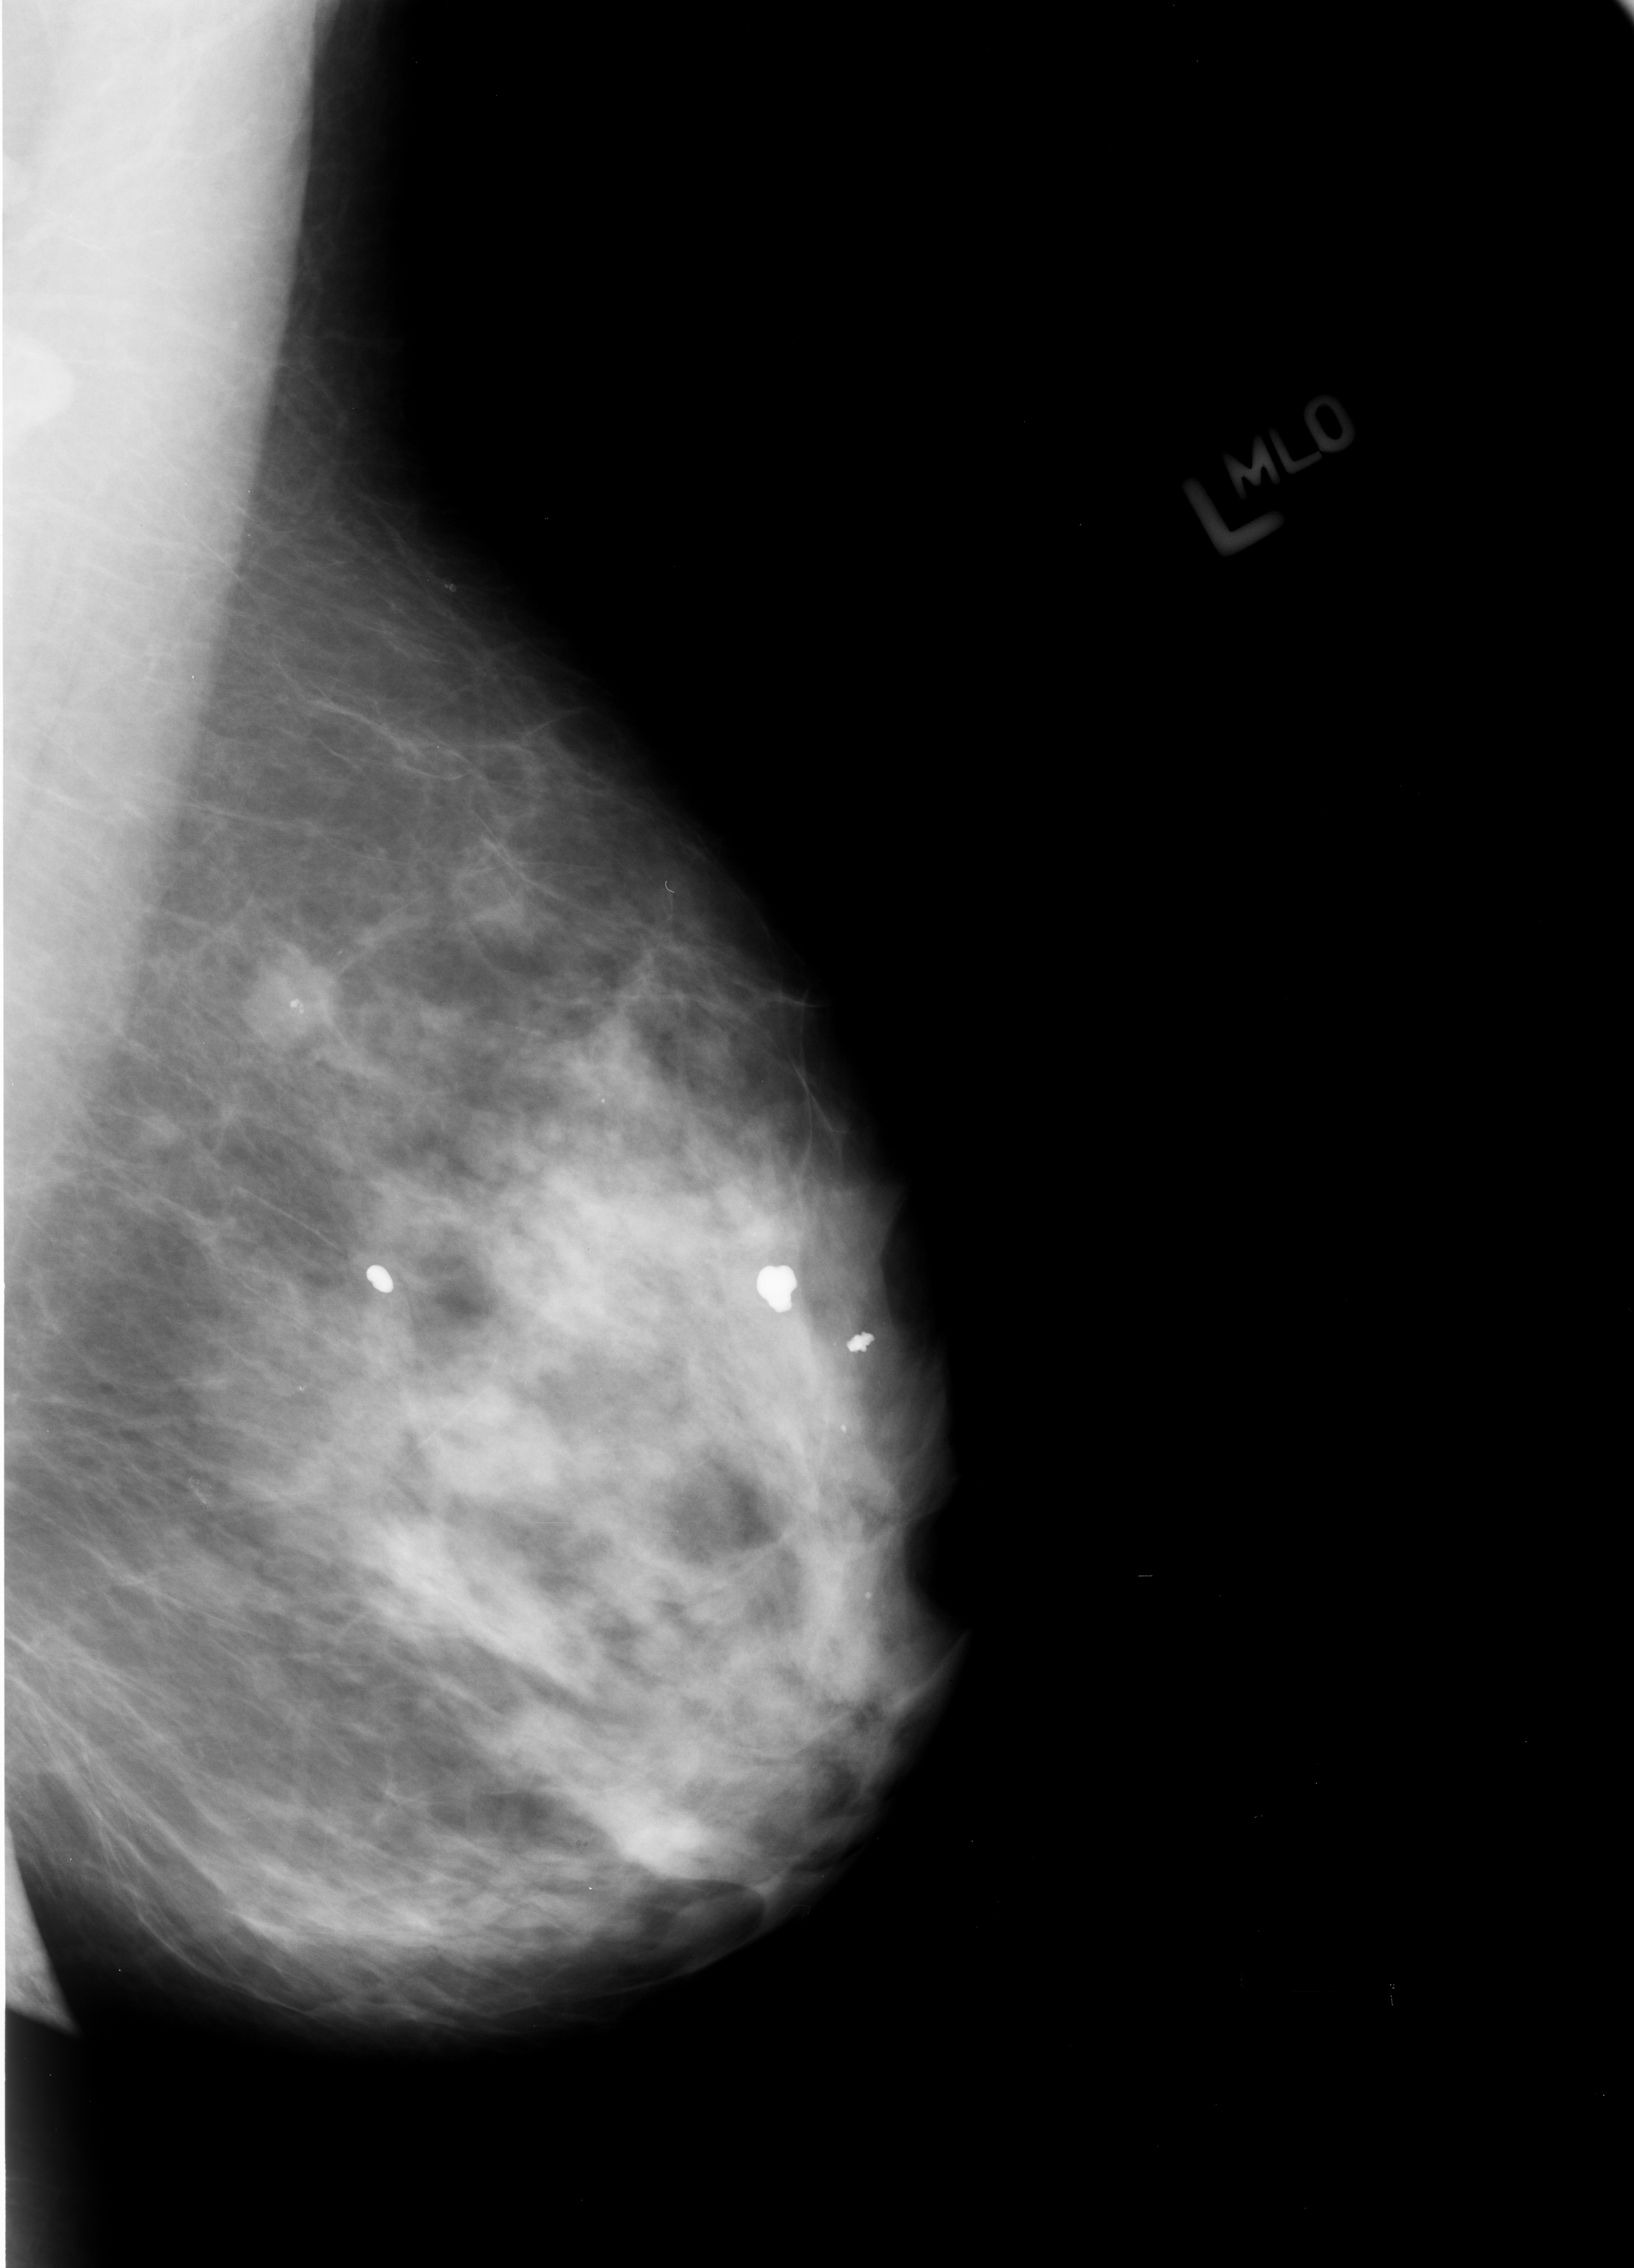
Mammogram (digitized film). Left breast. MLO view. BI-RADS breast density category 3 (scale 1–4). 1634 × 2268 image matrix.
Expert-marked regions of interest on this image (one box per marked abnormality):
- mass, shape irregular, margins ill defined / spiculated; BI-RADS assessment category 4; pathology (as recorded): malignant: bounding box [x1, y1, x2, y2] px = [245, 948, 346, 1045]